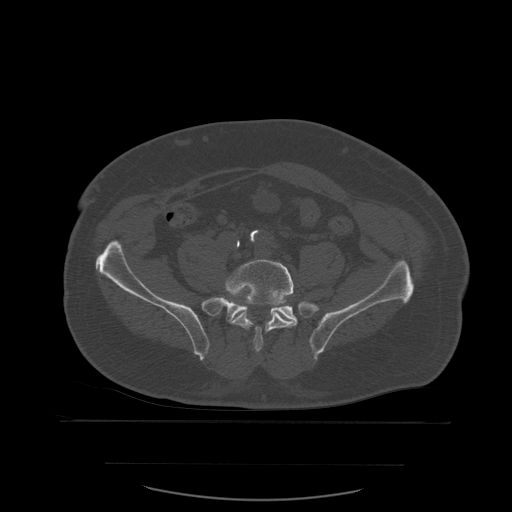
CT including the spine, one axial slice. Slice 130 of 590 in the series (ordered by position). Bone window (W 1800 / L 400 HU). 1.25 mm slice thickness. 512 × 512 image matrix, field of view 479 × 479 mm. Patient age 71 years. From the clinical record (not read from this slice): primary cancer: lung; vertebrae with lytic lesions (as recorded): T1, T2, L5, S1.
Annotated regions visible in this slice (semi-automatic segmentation, software-assisted and operator-edited):
- L5 vertebra: bounding box [x1, y1, x2, y2] px = [225, 260, 296, 353]